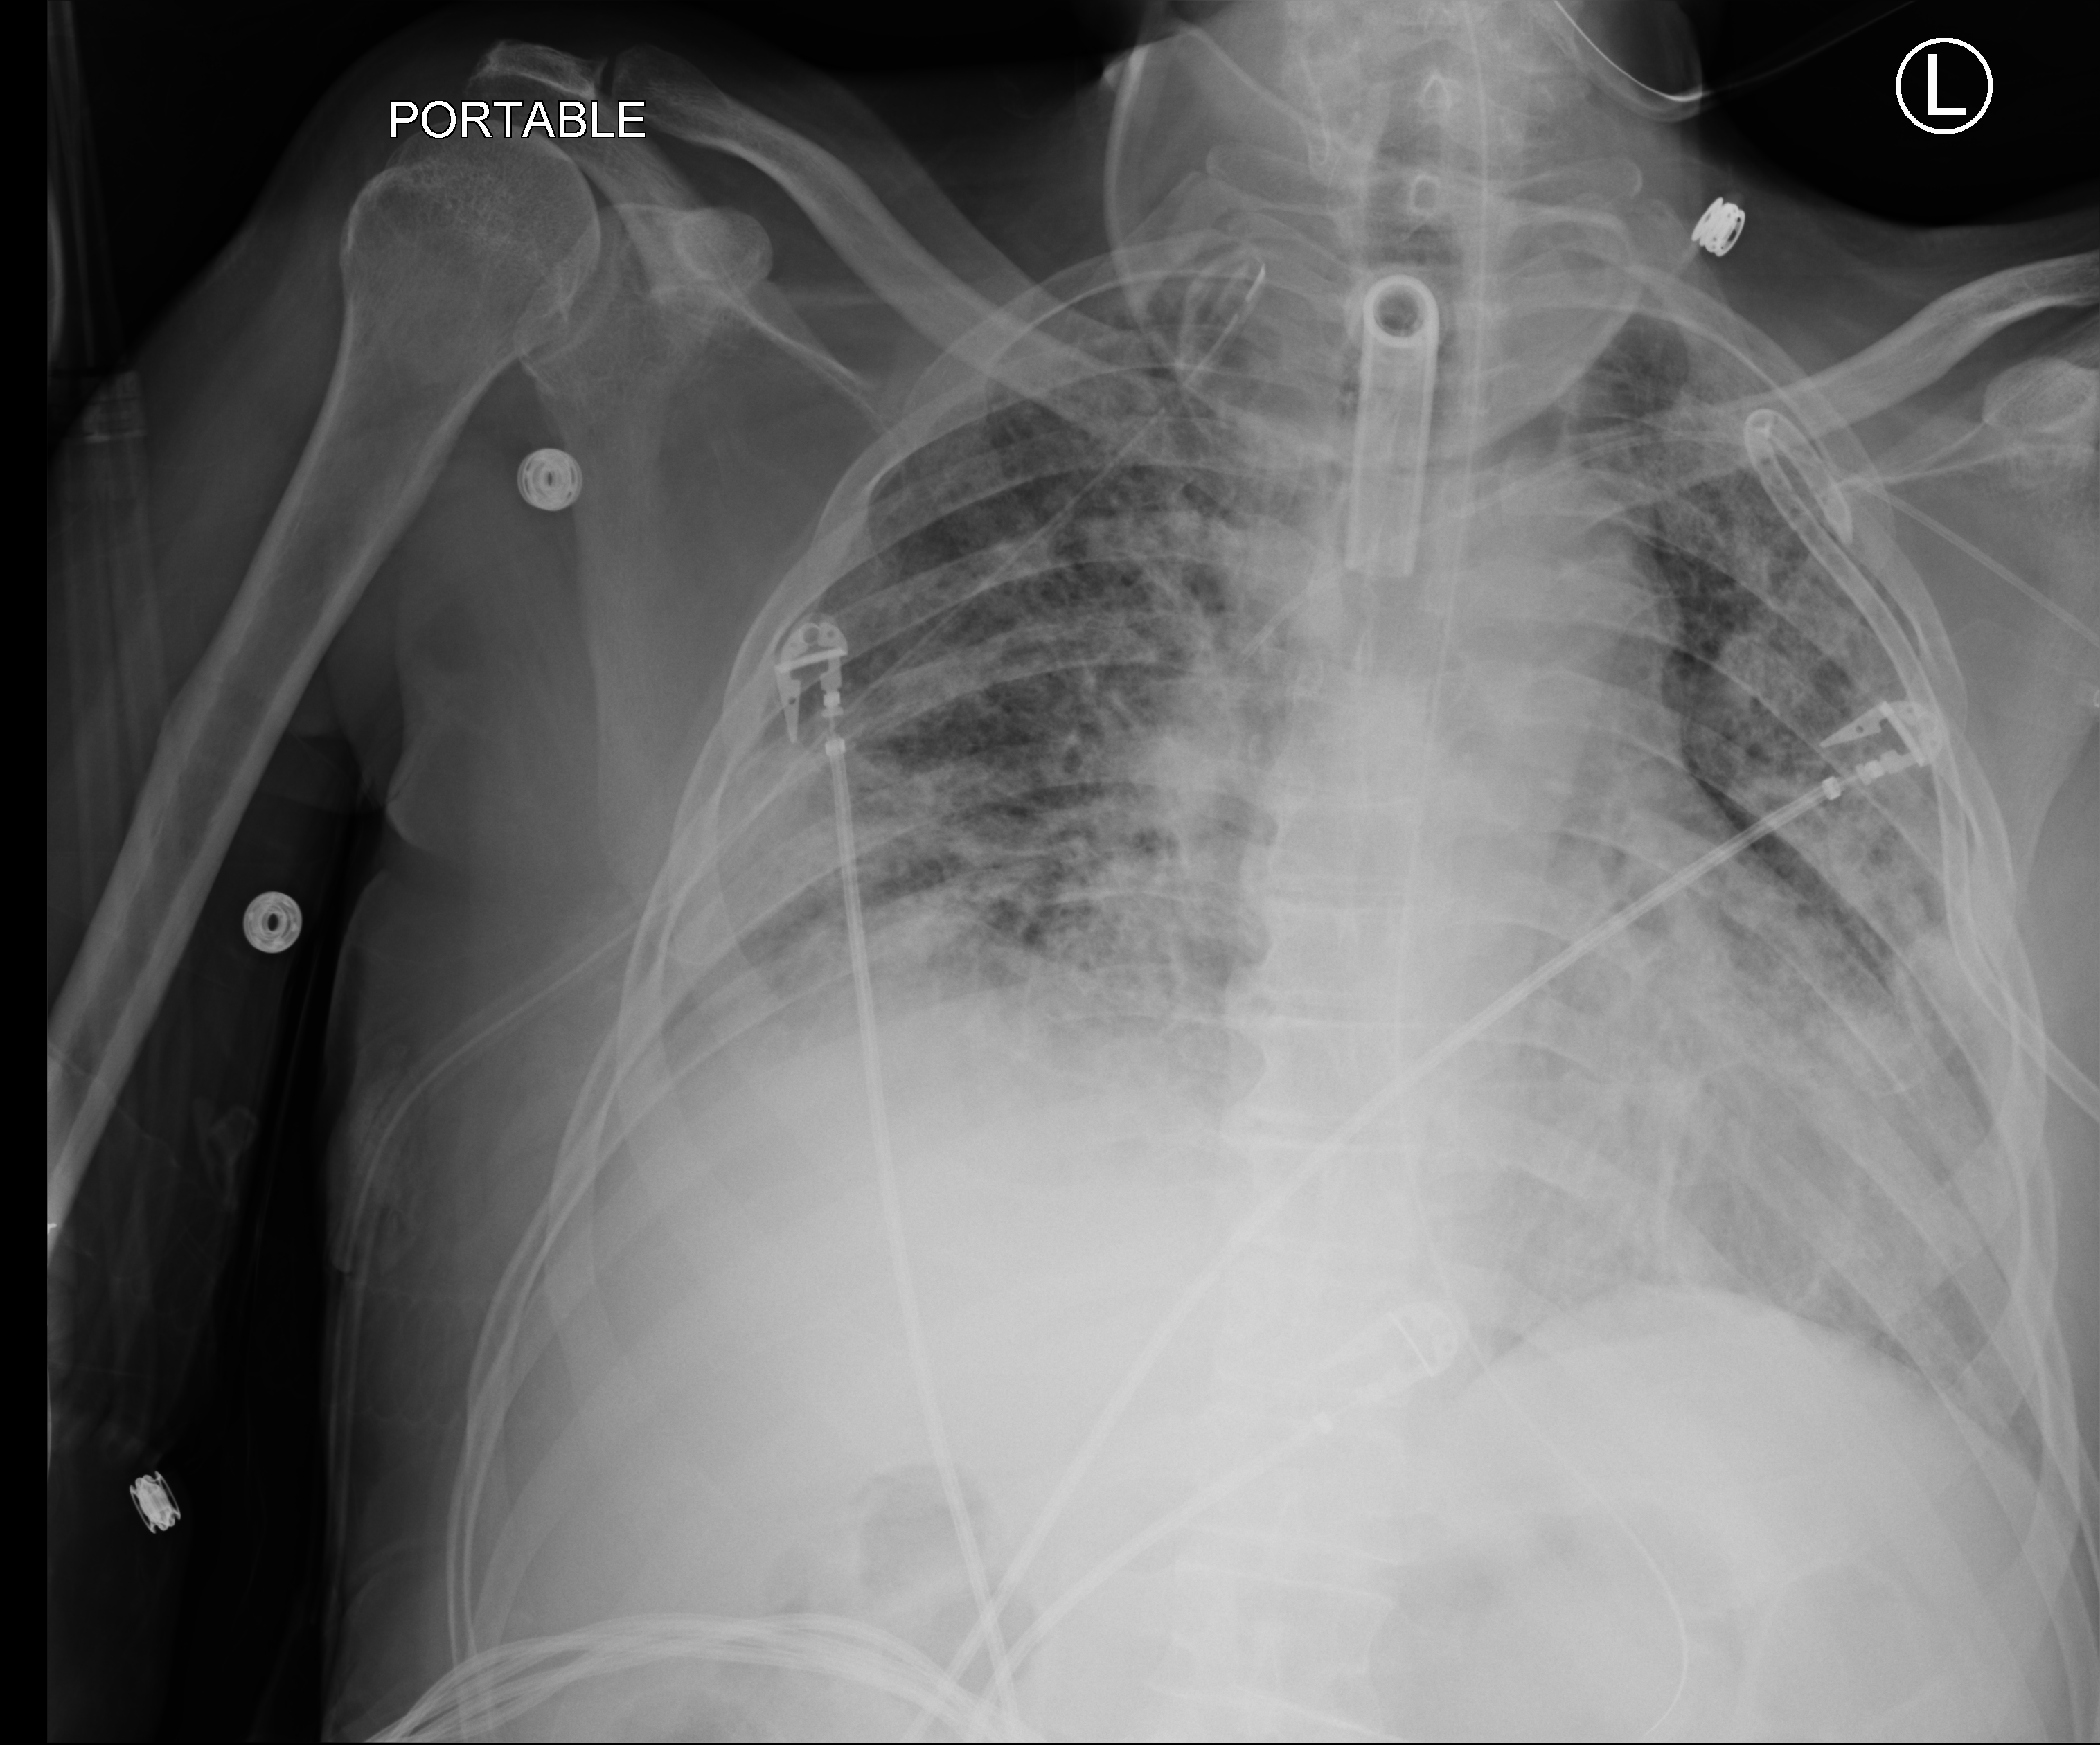
Bedside chest radiograph (computed radiography); anteroposterior (AP) projection. Male patient hospitalised with COVID-19, age 18–59 years.
Admission-level facts for this patient (not findings on this image; timing relative to this image not recorded): COPD (admission record): no; smoking status (admission record): never.